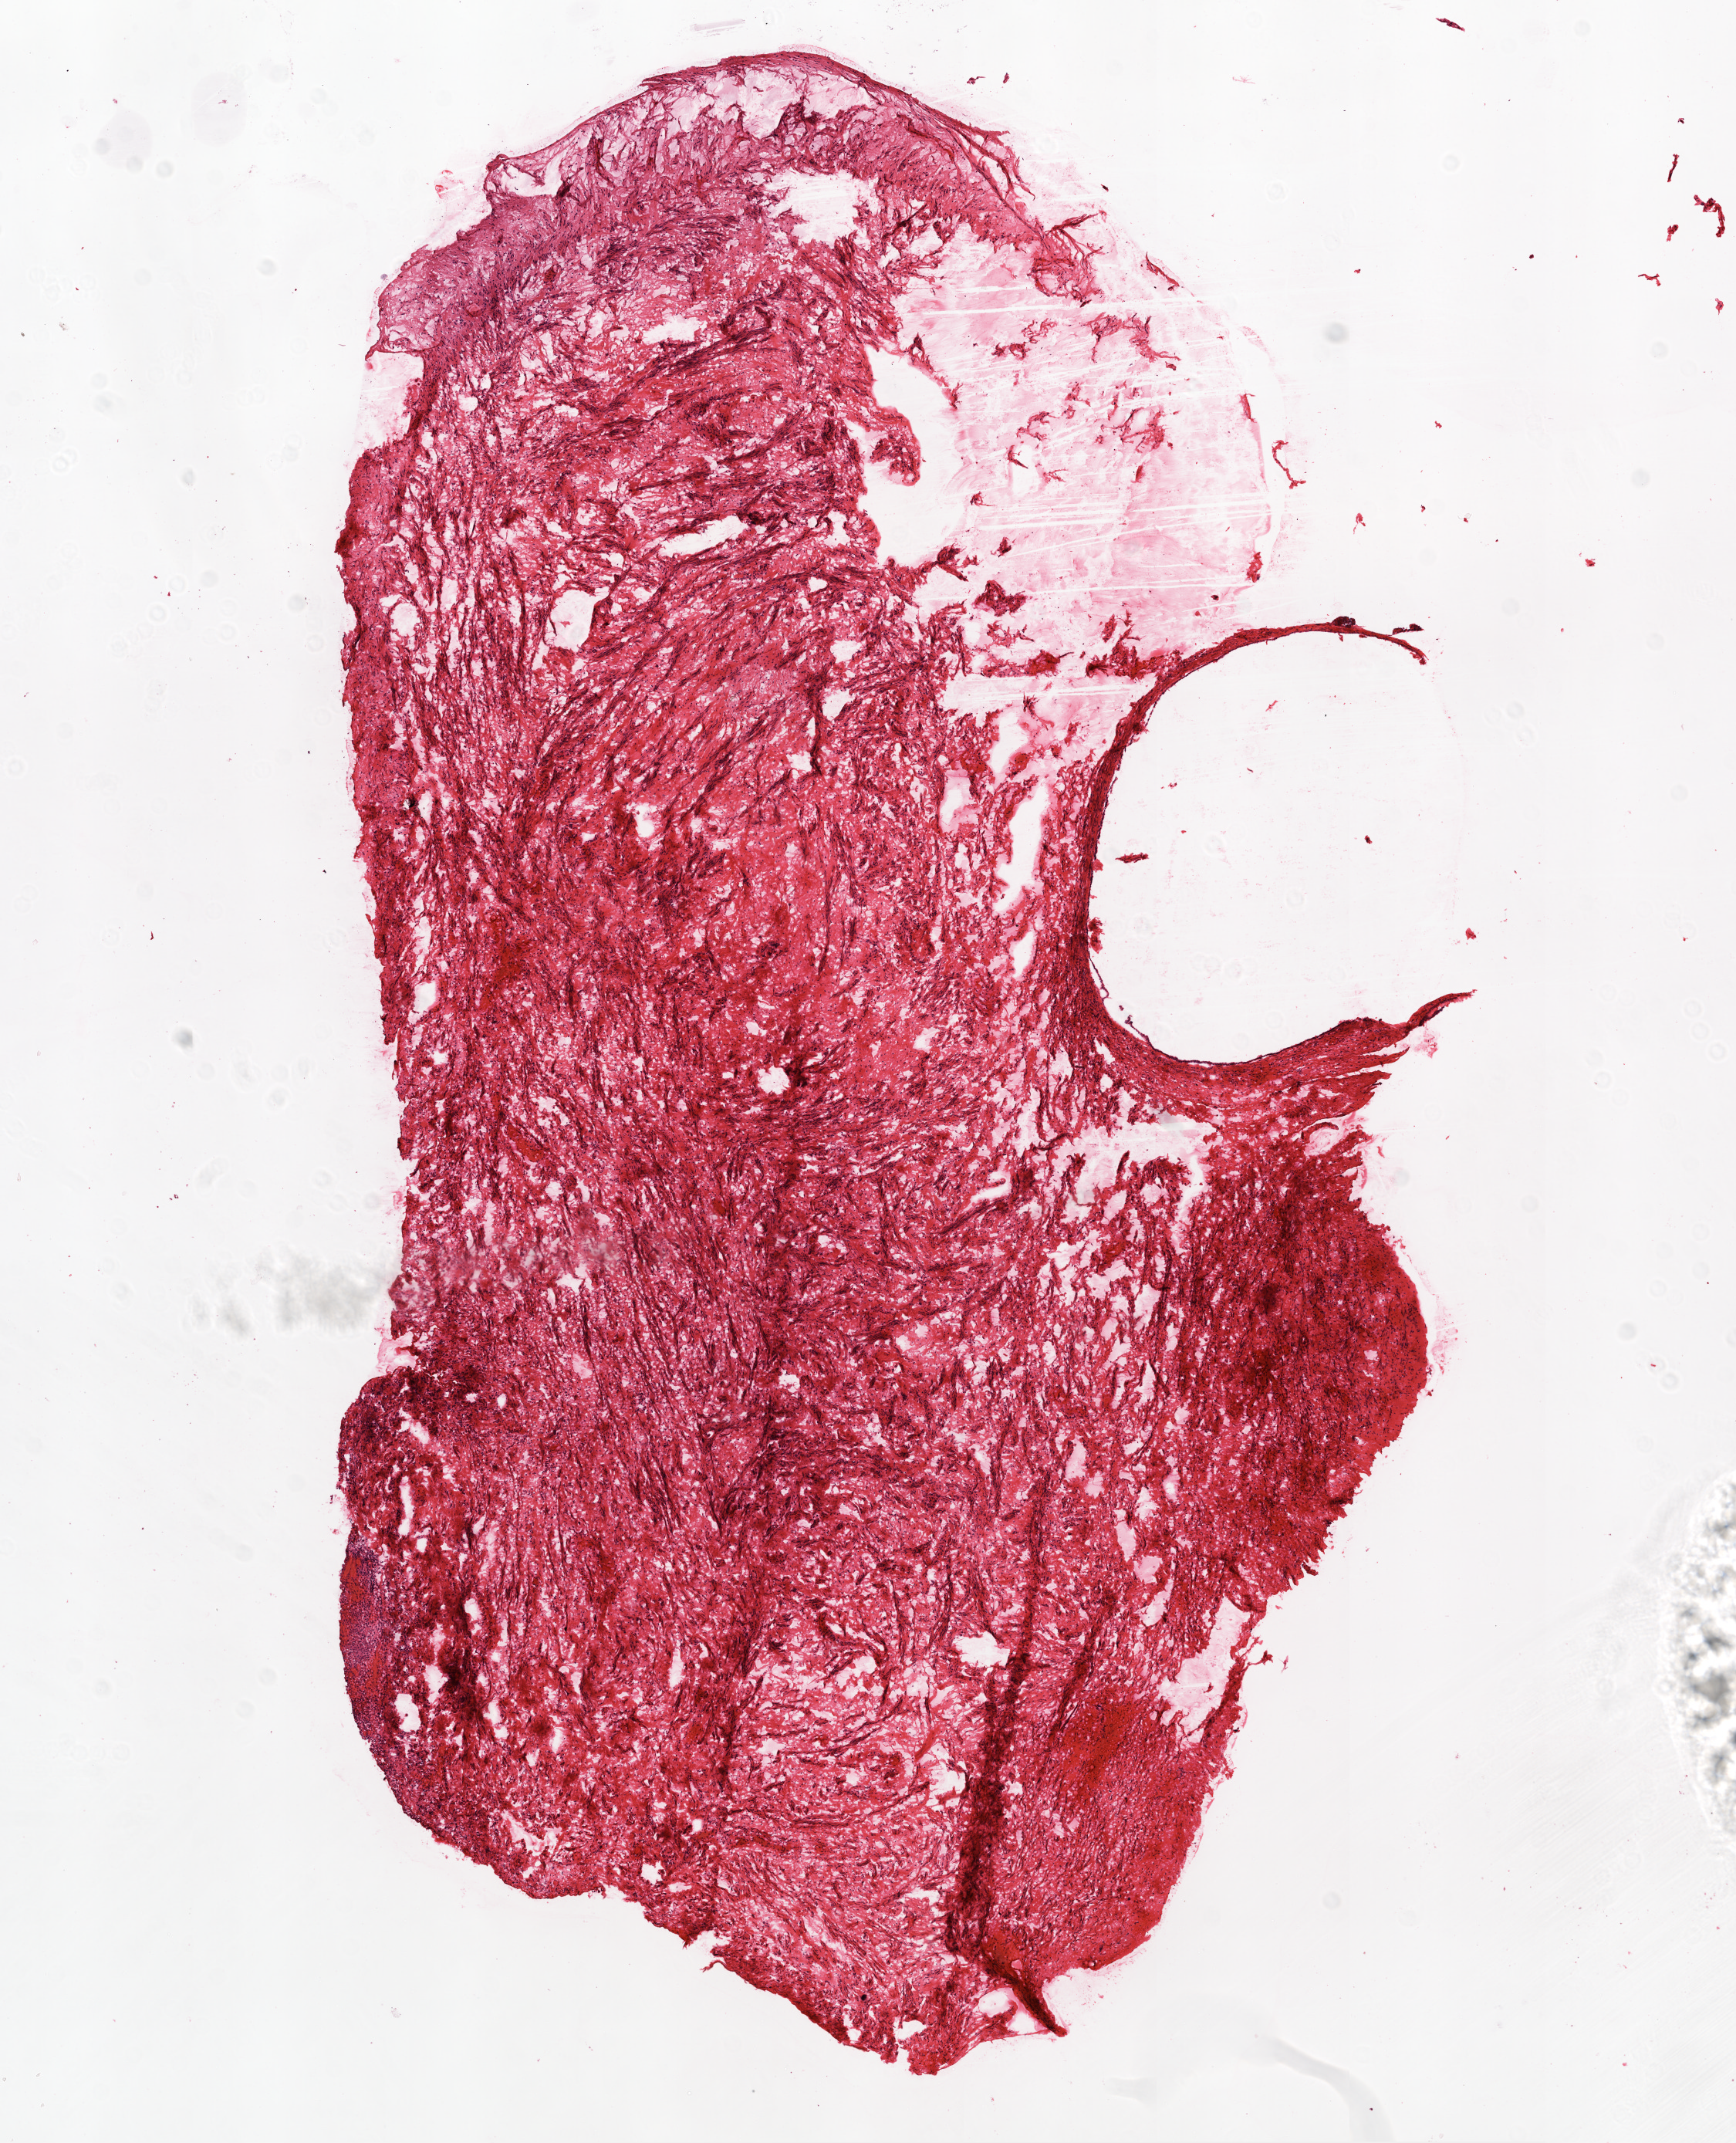
Whole-slide histology image, Hematoxylin and eosin (H&E) stained — a low-resolution overview of the entire scanned area, about 9.0 x 11.1 mm (slide scanned at 20x), frozen section, solid tissue normal (non-tumour tissue) sample from the ovary. Female patient; age at initial diagnosis 63 years.
This section: solid tissue normal sample (biorepository sample class). Patient diagnosis: Serous cystadenocarcinoma, NOS.